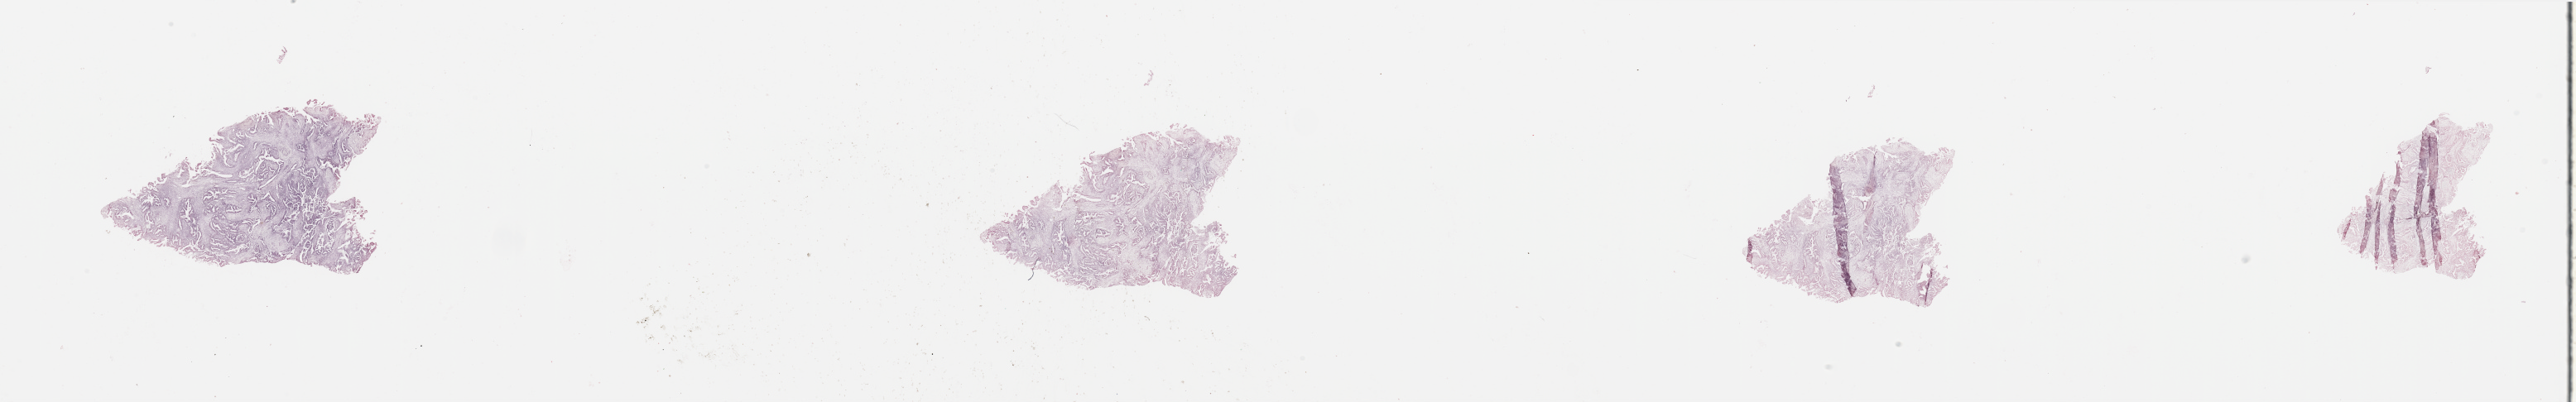
Digitized H&E-stained tissue section (whole slide) — shown as a low-resolution overview of the whole scanned area (about 49.2 x 7.7 mm, slide scanned at 20x), tumour tissue sample, uterus. Patient: female, age 58 years.
Diagnosis: Endometrioid adenocarcinoma, NOS.